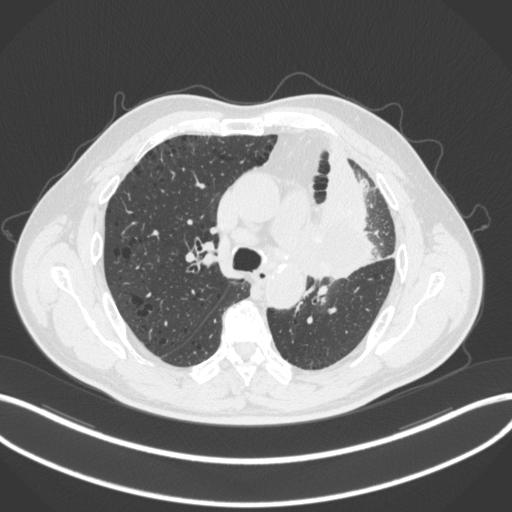
Chest CT, one axial slice. Position 189 of 286 along the scan axis. Lung window (W 1500 / L -600 HU). 1 mm slice thickness. 512 × 512 image matrix, field of view 400 × 400 mm. Patient: male, 68 years. Case-level facts recorded for this patient, not image findings: clinical TNM (as recorded): T3 N3 M1.
Annotated regions visible in this slice (bounding box drawn by a radiologist):
- lung tumour (recorded histology: adenocarcinoma): bounding box (x1, y1, x2, y2) in pixels: (315, 195, 375, 282)